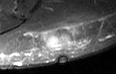
MRI of an extremity soft-tissue mass, one axial slice; position 12 of 36 along the scan axis; STIR; MR volume resampled by the dataset authors to the PET/CT grid (not the native acquisition matrix); 3.27 mm slice thickness; 116 × 74 image matrix, field of view 113 × 72 mm. Male patient. From the clinical record (not read from this slice): histological type: pleiomorphic leiomyosarcoma; grade: high; site of the primary tumour: left buttock.
Outlined on this slice (expert contour drawn on MRI and transferred to this co-registered scan by the dataset authors):
- gross tumour volume including surrounding oedema: bounding box <37,24,74,50> (left, top, right, bottom; pixels)
- gross tumour volume (mass): <43,29,72,49>